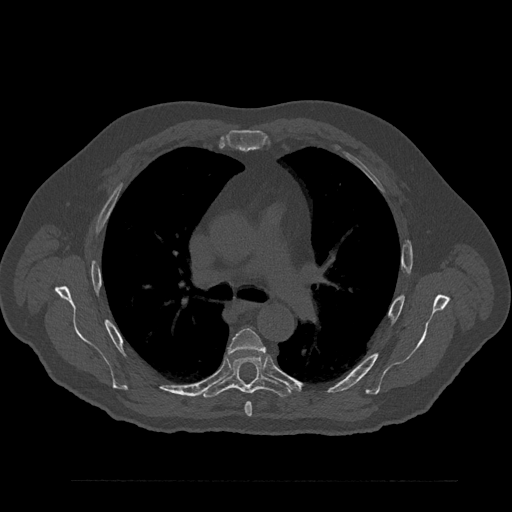
CT including the spine, one axial slice; slice 573 of 797 in the series (ordered by position); 120 kVp; bone window (W 1800 / L 400 HU); 0.5 mm slice thickness; 512 × 512 image matrix, field of view 430 × 430 mm. Male patient, age 61 years. From the clinical record (not read from this slice): primary cancer: prostate.
Outlined on this slice (semi-automatic segmentation, software-assisted and operator-edited):
- T5 vertebra: bounding box <228,328,266,416> (left, top, right, bottom; pixels)
- T6 vertebra: <201,353,294,398>